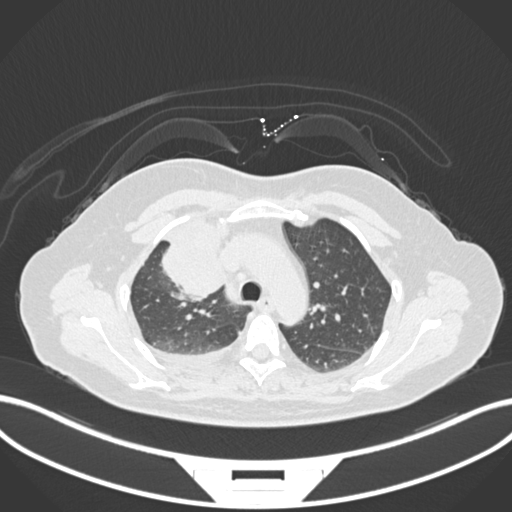
Chest CT, one axial slice. Slice 116 of 172 in the series (ordered by position). Reconstruction kernel B30f. Lung window (W 1500 / L -600 HU). 1 mm slice thickness. 512 × 512 image matrix. Female patient, age 52 years. Case-level facts recorded for this patient, not image findings: clinical TNM (as recorded): T3 N1 M1.
Outlined on this slice (rectangle marked by the reading radiologist):
- lung tumour (recorded histology: adenocarcinoma): bounding box [x1, y1, x2, y2] px = [155, 215, 231, 303]